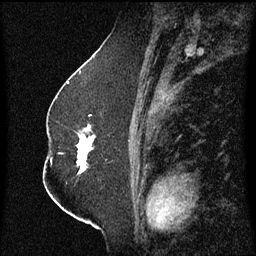
Breast MRI (dynamic contrast-enhanced), one sagittal slice; slice 33 of 60 in the series (ordered by position); dynamic contrast-enhanced series, image 2 of 3 at this slice position (ordered by acquisition); 1.5 T; TE 4.2 ms, TR 8.4 ms; 256 × 256 image matrix, field of view 200 × 200 mm. Female patient, age 52 years. Case-level facts recorded for this patient, not image findings: setting: breast cancer imaged before/during neoadjuvant chemotherapy; receptor status: HR-positive, HER2-negative.
Structures marked on this image (semi-automatically segmented with operator editing):
- analysis volume of interest (the breast-tissue region the enhancement analysis was run in; not a lesion): bounding box <78,116,97,175> (left, top, right, bottom; pixels)
- tumour enhancement mask (voxels above the 70 % enhancement threshold inside the analysis volume of interest): <78,124,96,173>